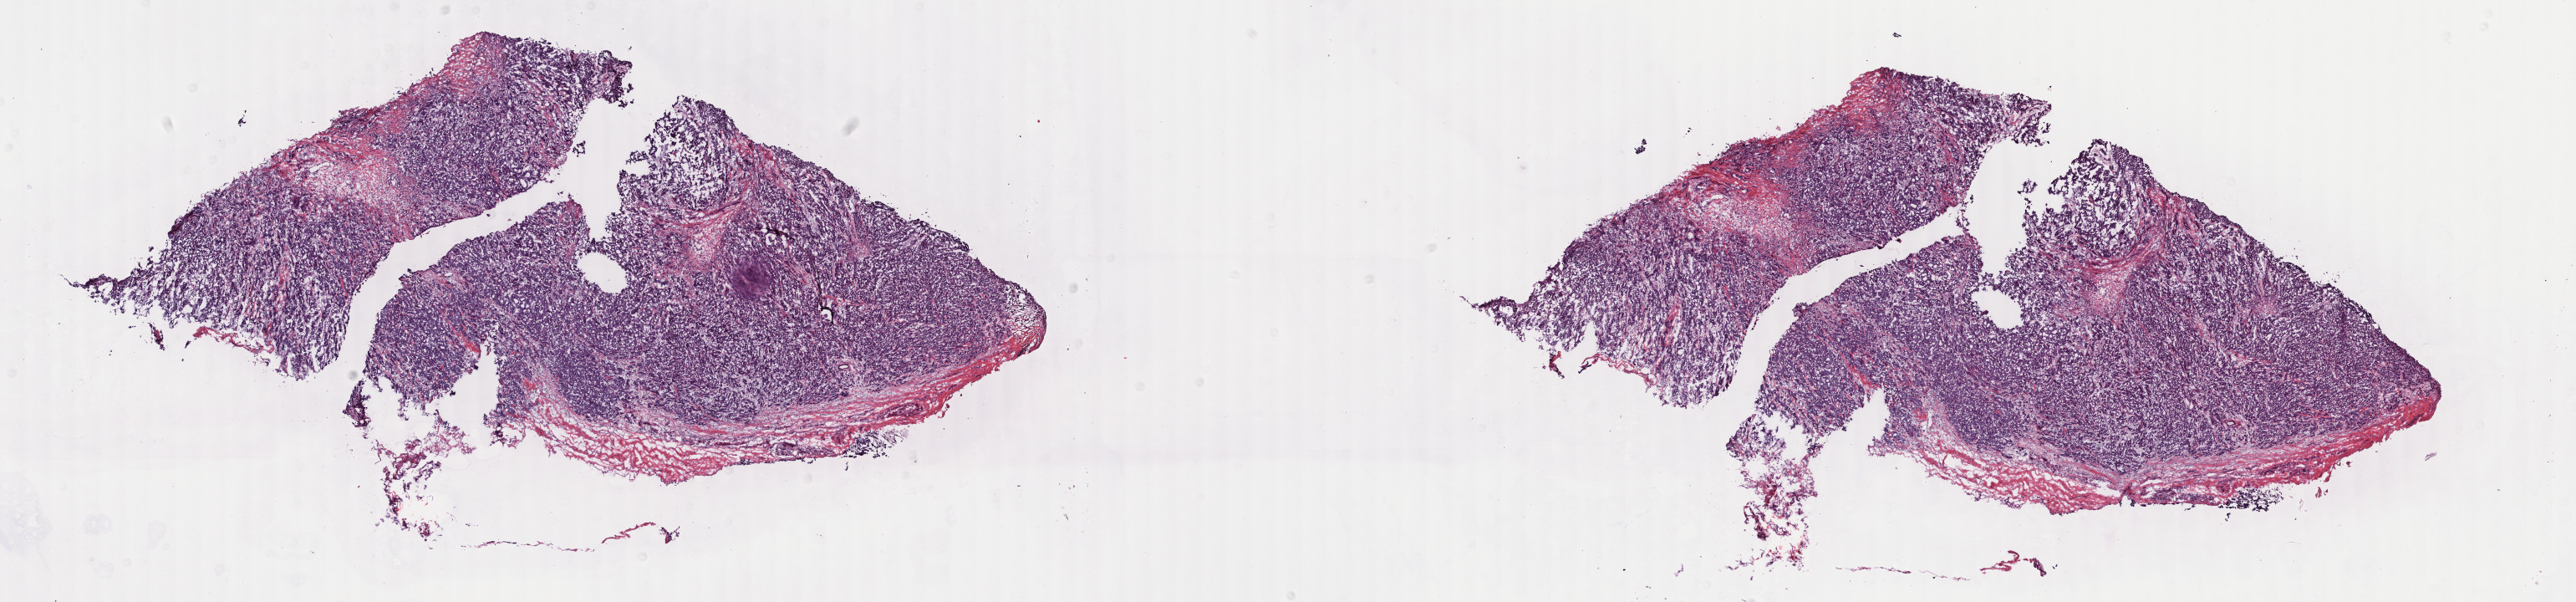
Digitized H&E tissue section (whole slide) — a low-resolution overview of the entire scanned area, about 24.5 x 5.7 mm; frozen section; primary tumour sample from the breast. Female patient; age at initial diagnosis 62 years. Slide review estimates, as recorded: tumour cells 70%, tumour nuclei 80%, normal cells 0%, stromal cells 27%, necrosis 3%. Inflammatory infiltration, as recorded: lymphocyte infiltration 10%, monocyte infiltration 1%, neutrophil infiltration 0%.
Pathologic diagnosis: Infiltrating duct carcinoma, NOS. Lymph nodes positive (case pathology): 0 of 1 examined. Laterality: right. TNM: T1 N0 (i-) M0. AJCC pathologic stage: IA.